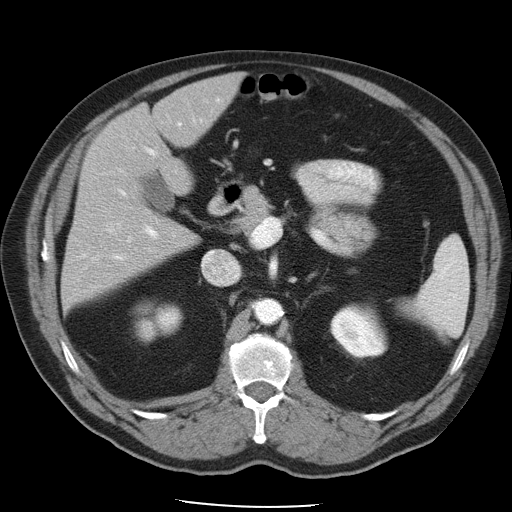
Contrast-enhanced abdominal CT, one axial slice; position 27 of 49 along the scan axis; intravenous contrast given; soft-tissue window (W 400 / L 40 HU); 5 mm slice thickness; 512 × 512 image matrix, field of view 395 × 395 mm. Male patient, age 68 years. Case-level facts recorded for this patient, not image findings: diagnosis: colorectal cancer liver metastases, imaged before liver resection; multiple liver metastases: yes; largest metastasis: 1.7 cm; chemotherapy before resection: yes.
Structures marked on this image (outlined manually by an expert reader):
- hepatic veins: box from (x=108, y=167) to (x=239, y=284) px
- liver: (x=62, y=75)–(x=240, y=307)
- planned liver remnant (the part of the liver to remain after resection): (x=64, y=75)–(x=241, y=307)
- portal vein (with intrahepatic branches): (x=83, y=98)–(x=220, y=261)